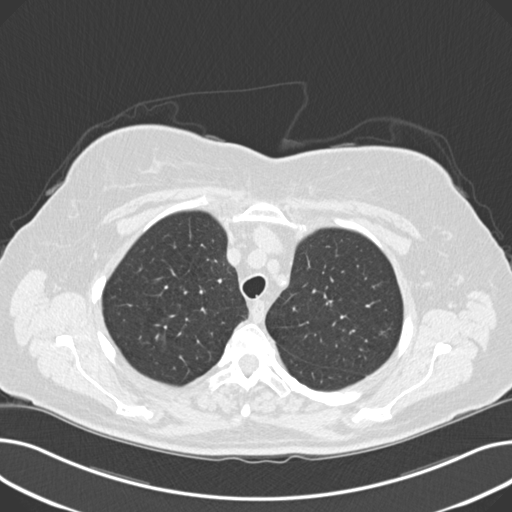
Low-dose screening chest CT, axial slice, third screening round (two years after baseline), lung window (W 1500 / L -600 HU), 120 kVp, slice 48 of 203 in the series, 512 × 512 image matrix. Female participant, aged 60 years at enrolment. Current smoker at enrolment.
Expert-annotated lung lesion, box from (x=368, y=318) to (x=403, y=354) px. The screening reader recorded 8 non-calcified nodules or masses ≥4 mm on this exam (right upper lobe, lingula, lingula, right middle lobe, right lower lobe, left lower lobe, left lower lobe, left lower lobe); which of them this box marks is not recorded.